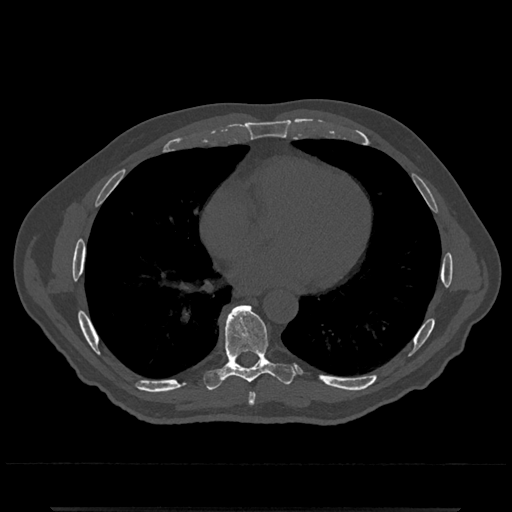
CT including the spine, one axial slice. Slice 670 of 797 in the series (ordered by position). Reconstruction kernel Br40s/3. Bone window (W 1800 / L 400 HU). 0.5 mm slice thickness. 512 × 512 image matrix, field of view 393 × 393 mm. Patient: male, 67 years. Case-level facts recorded for this patient, not image findings: primary cancer: prostate.
Structures marked on this image (semi-automatic segmentation, software-assisted and operator-edited):
- T7 vertebra: bounding box [x1, y1, x2, y2] px = [248, 392, 256, 405]
- T8 vertebra: [203, 305, 295, 390]